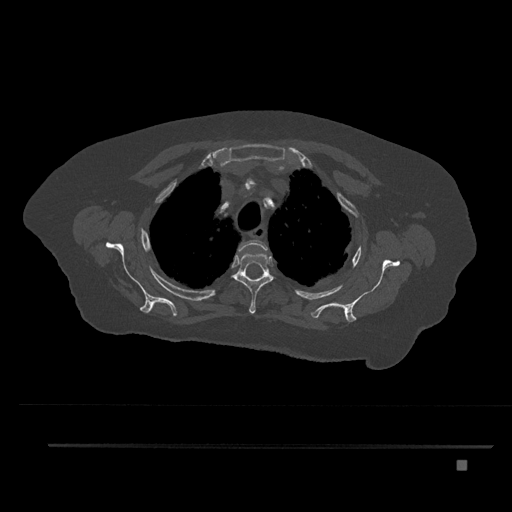
CT including the spine, one axial slice. Position 638 of 797 along the scan axis. Reconstruction kernel Br40s/3. 120 kVp. Bone window (W 1800 / L 400 HU). 0.5 mm slice thickness. 512 × 512 image matrix. Female patient, age 76 years. From the clinical record (not read from this slice): primary cancer: lung; vertebrae with lytic lesions (as recorded): T11, L3.
Annotated regions visible in this slice (semi-automatic segmentation, software-assisted and operator-edited):
- T2 vertebra: box from (x=237, y=240) to (x=268, y=255) px
- T3 vertebra: (x=231, y=251)–(x=274, y=314)